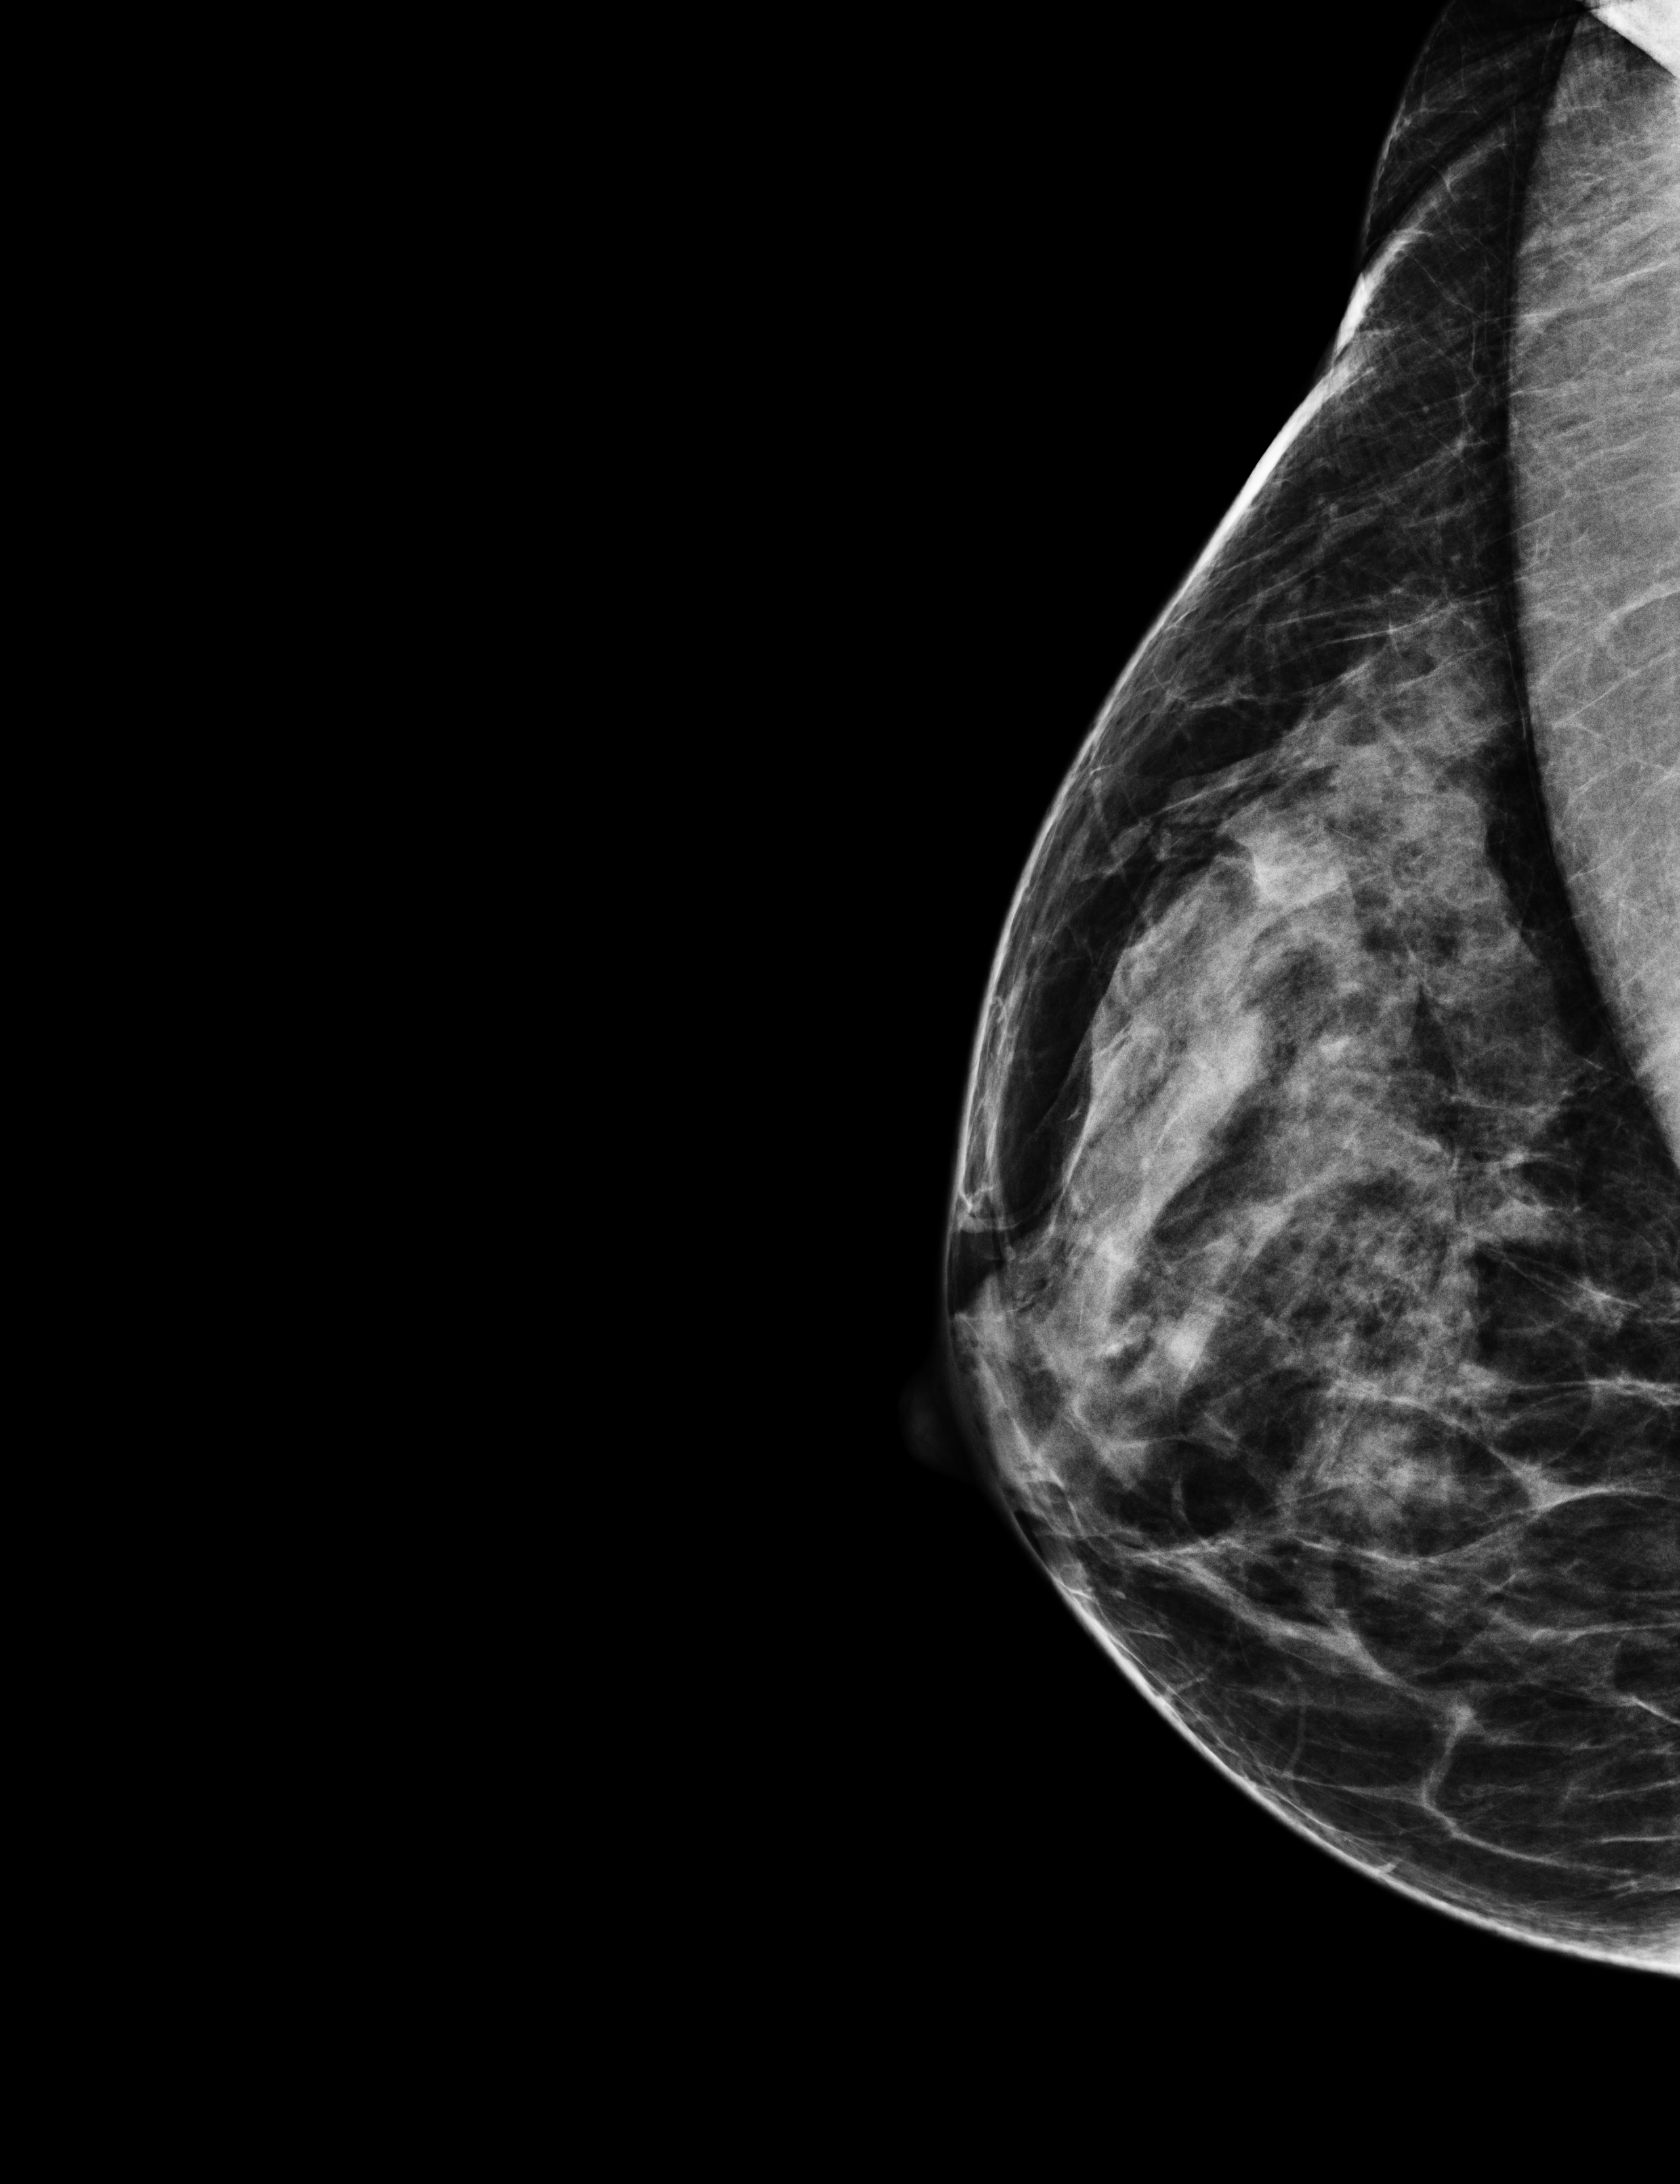
Digital mammogram (FFDM), right breast, laterally exaggerated craniocaudal (XCCL) view, screening examination, compressed breast thickness 53 mm, system: Selenia Dimensions. Patient: female, 47 years.
Breast density at the screening exam (both breasts): heterogeneously dense (BI-RADS density category c). Final BI-RADS category for the screening round (tomosynthesis exam, both breasts): category 2. Recall: no recall after this screen.